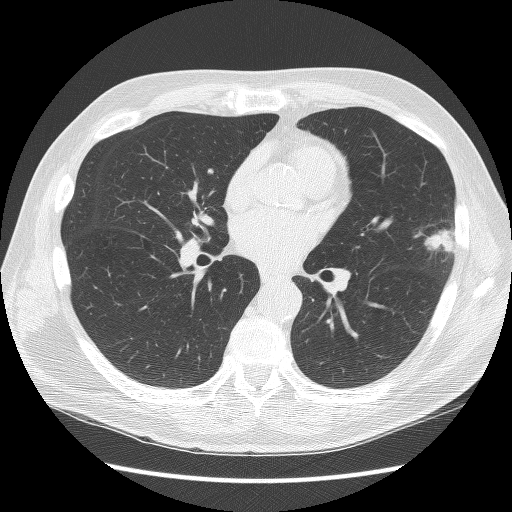
Axial slice from a low-dose chest CT screening exam. Third annual screen. Lung window (W 1500 / L -600 HU). 512 × 512 image matrix. Male participant, aged 67 years at enrolment.
- Expert-annotated lung lesion, box from (x=407, y=208) to (x=474, y=279) px.
- Screening reader's record for this exam (one nodule recorded; not confirmed to be the boxed lesion): non-calcified nodule or mass ≥4 mm, left upper lobe, 22 × 17 mm, poorly defined margins, soft tissue attenuation, pre-existing on the prior screen: yes; interval growth: yes.
- Official screen result: positive, other.
- Participant outcome: lung cancer diagnosed 72 days after this screen — squamous cell carcinoma, NOS, left upper lobe, moderately differentiated (G2), stage IB (AJCC 6th edition), 25 mm at pathology.